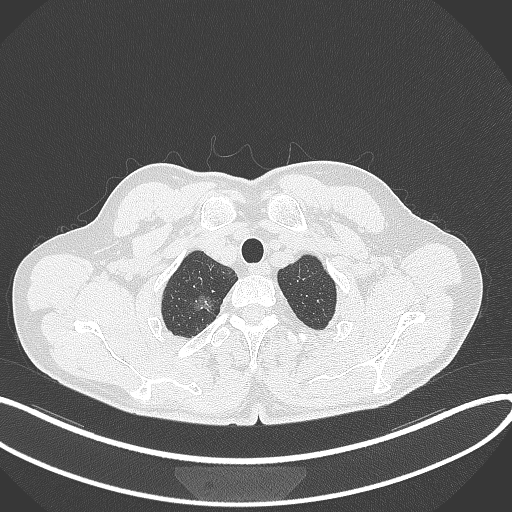
Chest CT, one axial slice; position 351 of 407 along the scan axis; reconstruction kernel B70f; 120 kVp; lung window (W 1500 / L -600 HU); 512 × 512 image matrix. Male patient, age 58 years. Case-level facts recorded for this patient, not image findings: clinical TNM (as recorded): T1c N0 M0.
Outlined on this slice (rectangle marked by the reading radiologist):
- lung tumour (recorded histology: adenocarcinoma): bounding box [x1, y1, x2, y2] px = [192, 288, 216, 318]